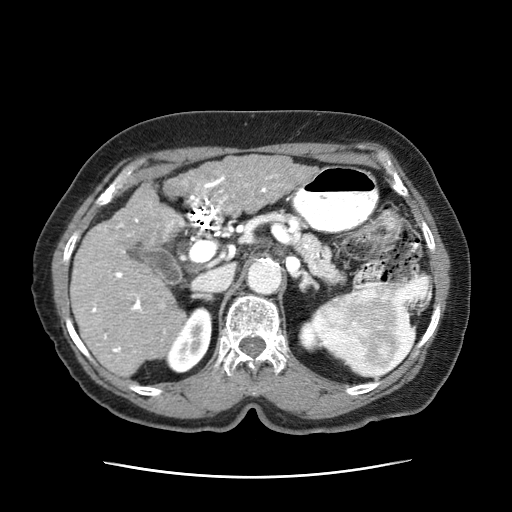
Contrast-enhanced abdominal CT (liver protocol), one axial slice. Position 31 of 63 along the scan axis. Soft-tissue window (W 400 / L 40 HU). 2.5 mm slice thickness. 512 × 512 image matrix, field of view 360 × 360 mm. Patient: female, 79 years. Case-level facts recorded for this patient, not image findings: diagnosis: hepatocellular carcinoma (patient treated with transarterial chemoembolisation; whether this scan precedes or follows treatment is not stated here); TNM stage (as recorded): Stage-II; Child-Pugh class: B; tumour nodularity: multinodular; tumour size: 5 cm.
Annotated regions visible in this slice (semi-automatically segmented with operator editing):
- abdominal aorta: bounding box (x1, y1, x2, y2) in pixels: (247, 257, 281, 294)
- liver parenchyma outside the tumour (the mass and vessels are separate outlines, so this box may not span the whole liver): (70, 182, 189, 380)
- mass: (165, 155, 319, 213)
- liver vessels: (91, 174, 233, 357)